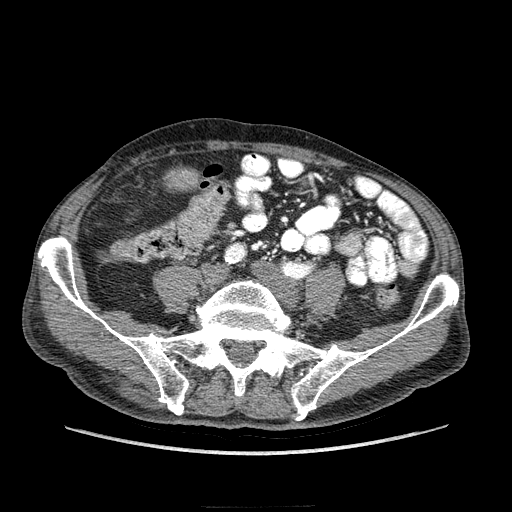
Contrast-enhanced abdominal CT (liver protocol), one axial slice; position 21 of 218 along the scan axis; reconstruction kernel STANDARD; soft-tissue window (W 400 / L 40 HU); 2.5 mm slice thickness; 512 × 512 image matrix, field of view 380 × 380 mm. Case-level facts recorded for this patient, not image findings: diagnosis: hepatocellular carcinoma (patient treated with transarterial chemoembolisation; whether this scan precedes or follows treatment is not stated here); TNM stage (as recorded): Stage-IIIA; Child-Pugh class: A; tumour differentiation: well differentiated; tumour nodularity: multinodular.
Structures marked on this image (semi-automatic segmentation, software-assisted and operator-edited):
- mass: bounding box (x1, y1, x2, y2) in pixels: (168, 168, 199, 189)